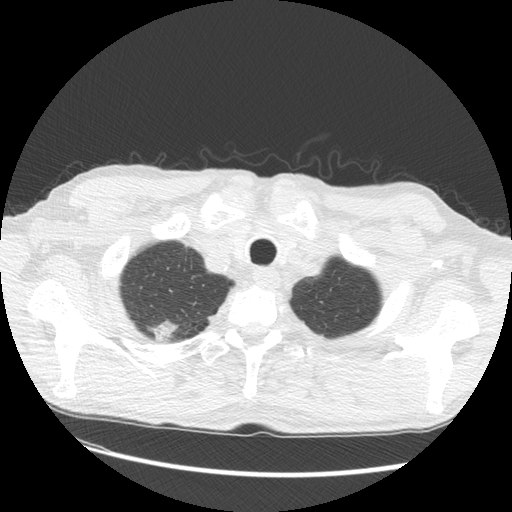
Low-dose screening chest CT, one axial slice; position 123 of 133 along the scan axis; lung window (W 1500 / L -600 HU); 2.5 mm slice thickness; 512 × 512 image matrix, field of view 360 × 360 mm.
Structures marked on this image (expert manual segmentation):
- lesion 2 (tumor, upper lobe of right lung): bounding box [x1, y1, x2, y2] px = [146, 319, 179, 342]